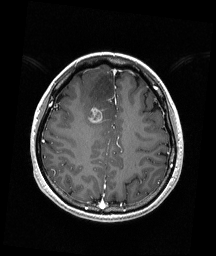
Brain MRI from a brain-tumour surgery series, one axial slice. Slice 60 of 192 in the series (ordered by position). T1-weighted post-contrast. 1 mm slice thickness. 216 × 256 image matrix. From the clinical record (not read from this slice): histopathology: Astrocytoma; WHO grade: 4; IDH mutation: yes.
Outlined on this slice (expert manual segmentation):
- tumour: bounding box (x1, y1, x2, y2) in pixels: (89, 107, 103, 124)